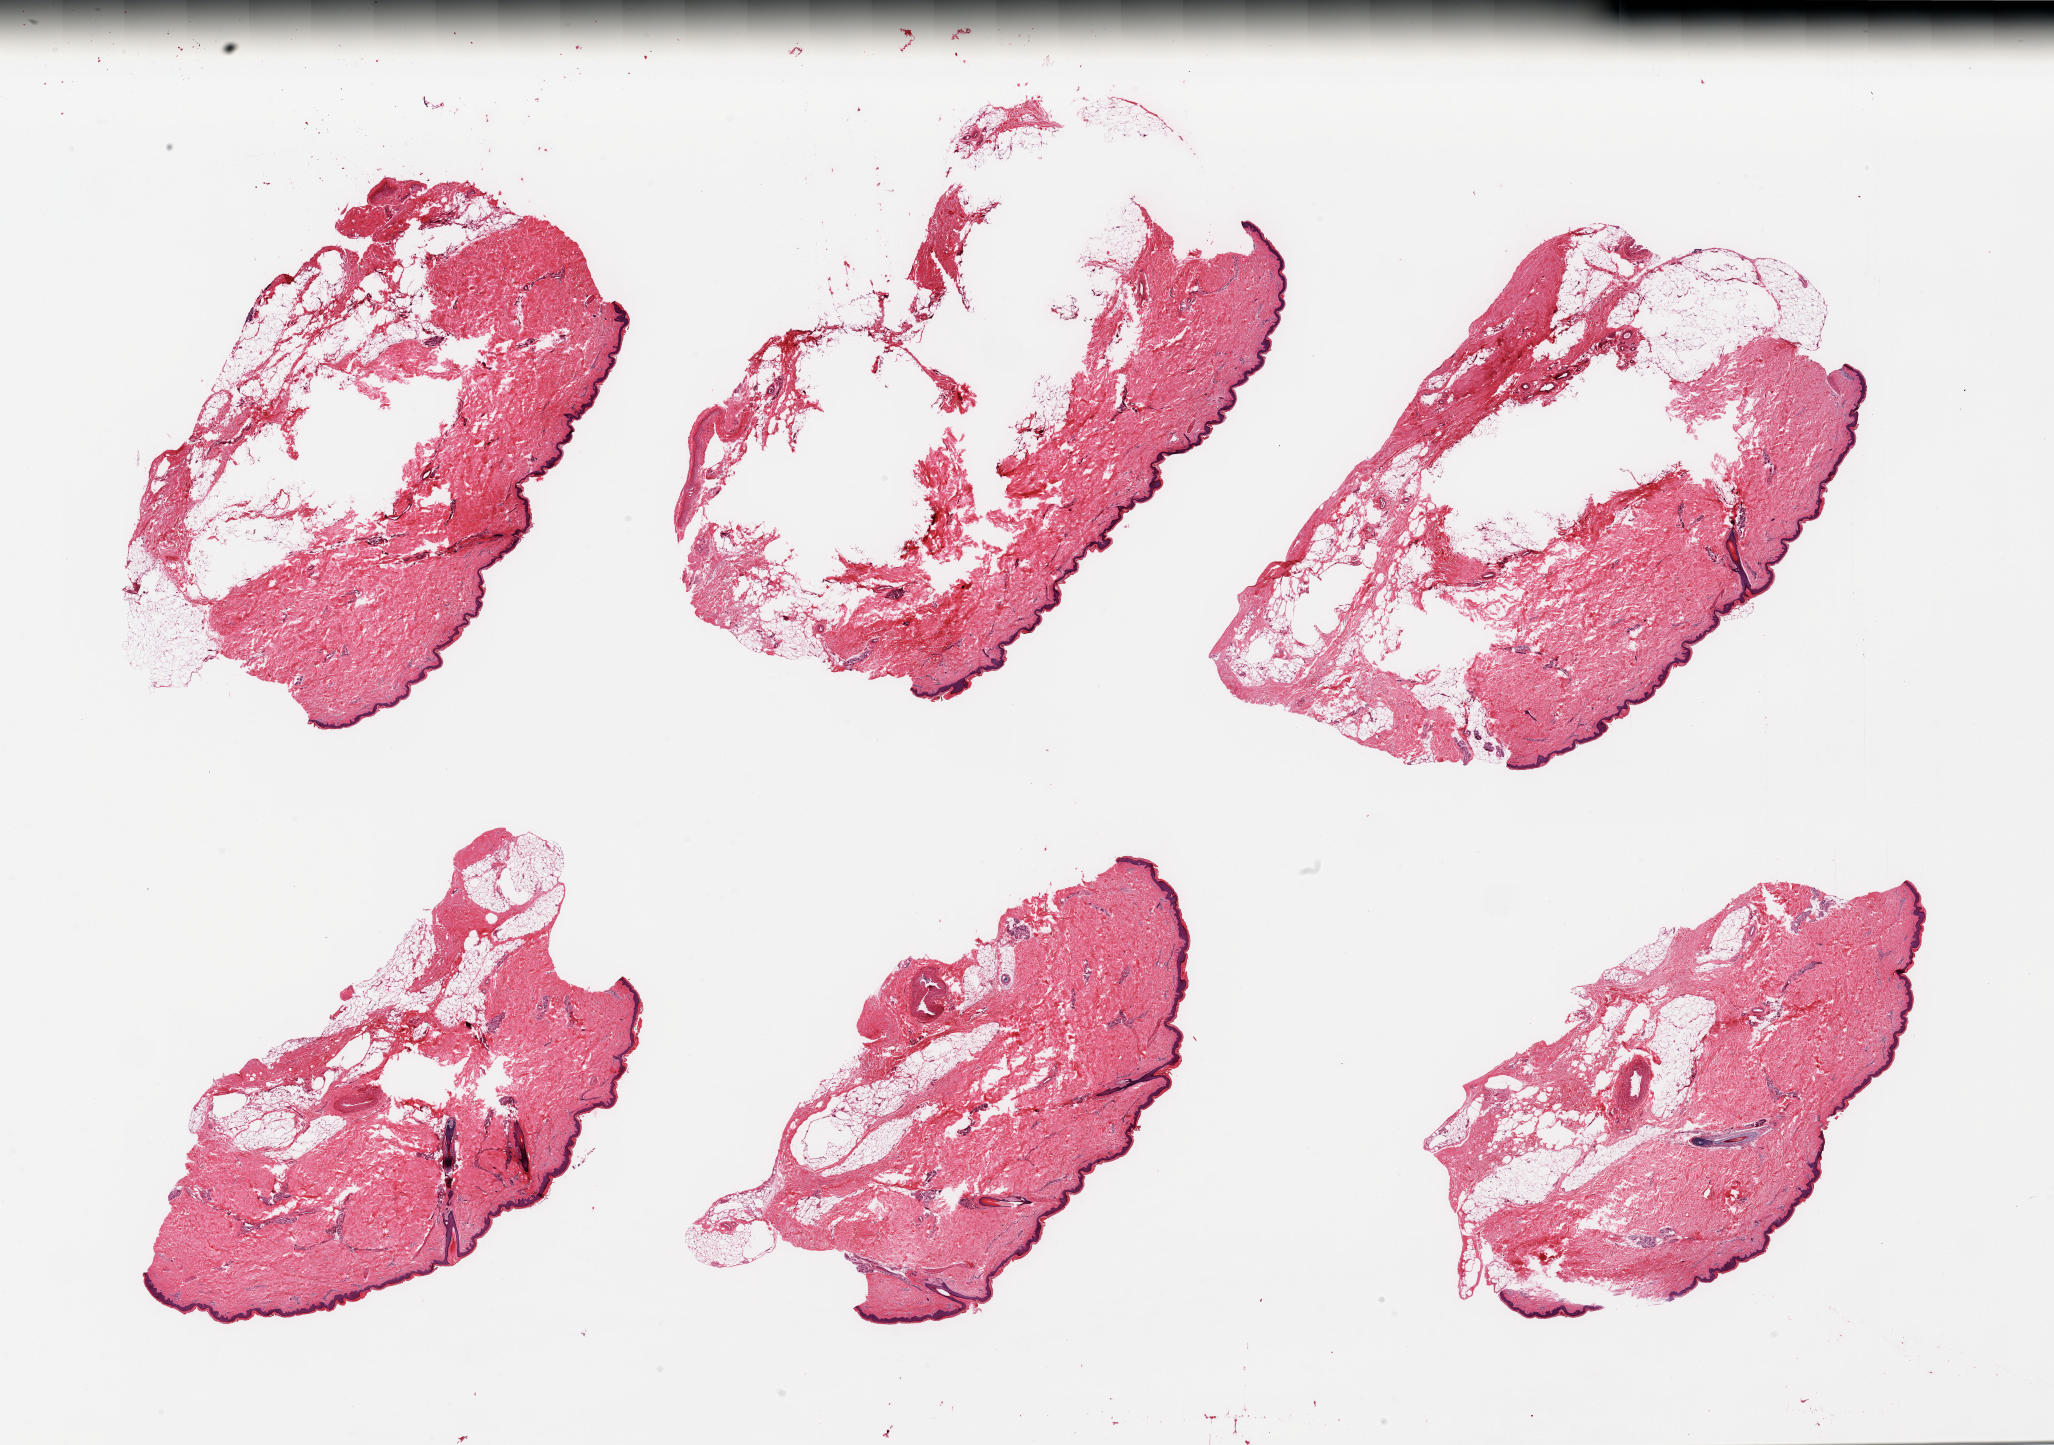
Haematoxylin and eosin whole-slide image, brightfield, a low-resolution overview of the entire scanned area, about 32.5 x 22.9 mm (acquisition: 20x scan); PAXgene-fixed, paraffin-embedded tissue; section of skin of lower leg (target tissue); tissue donor sample. Male donor.
Reviewer comment on this tissue sample: 6 fragmented pieces; up to 40% dermal fat content.